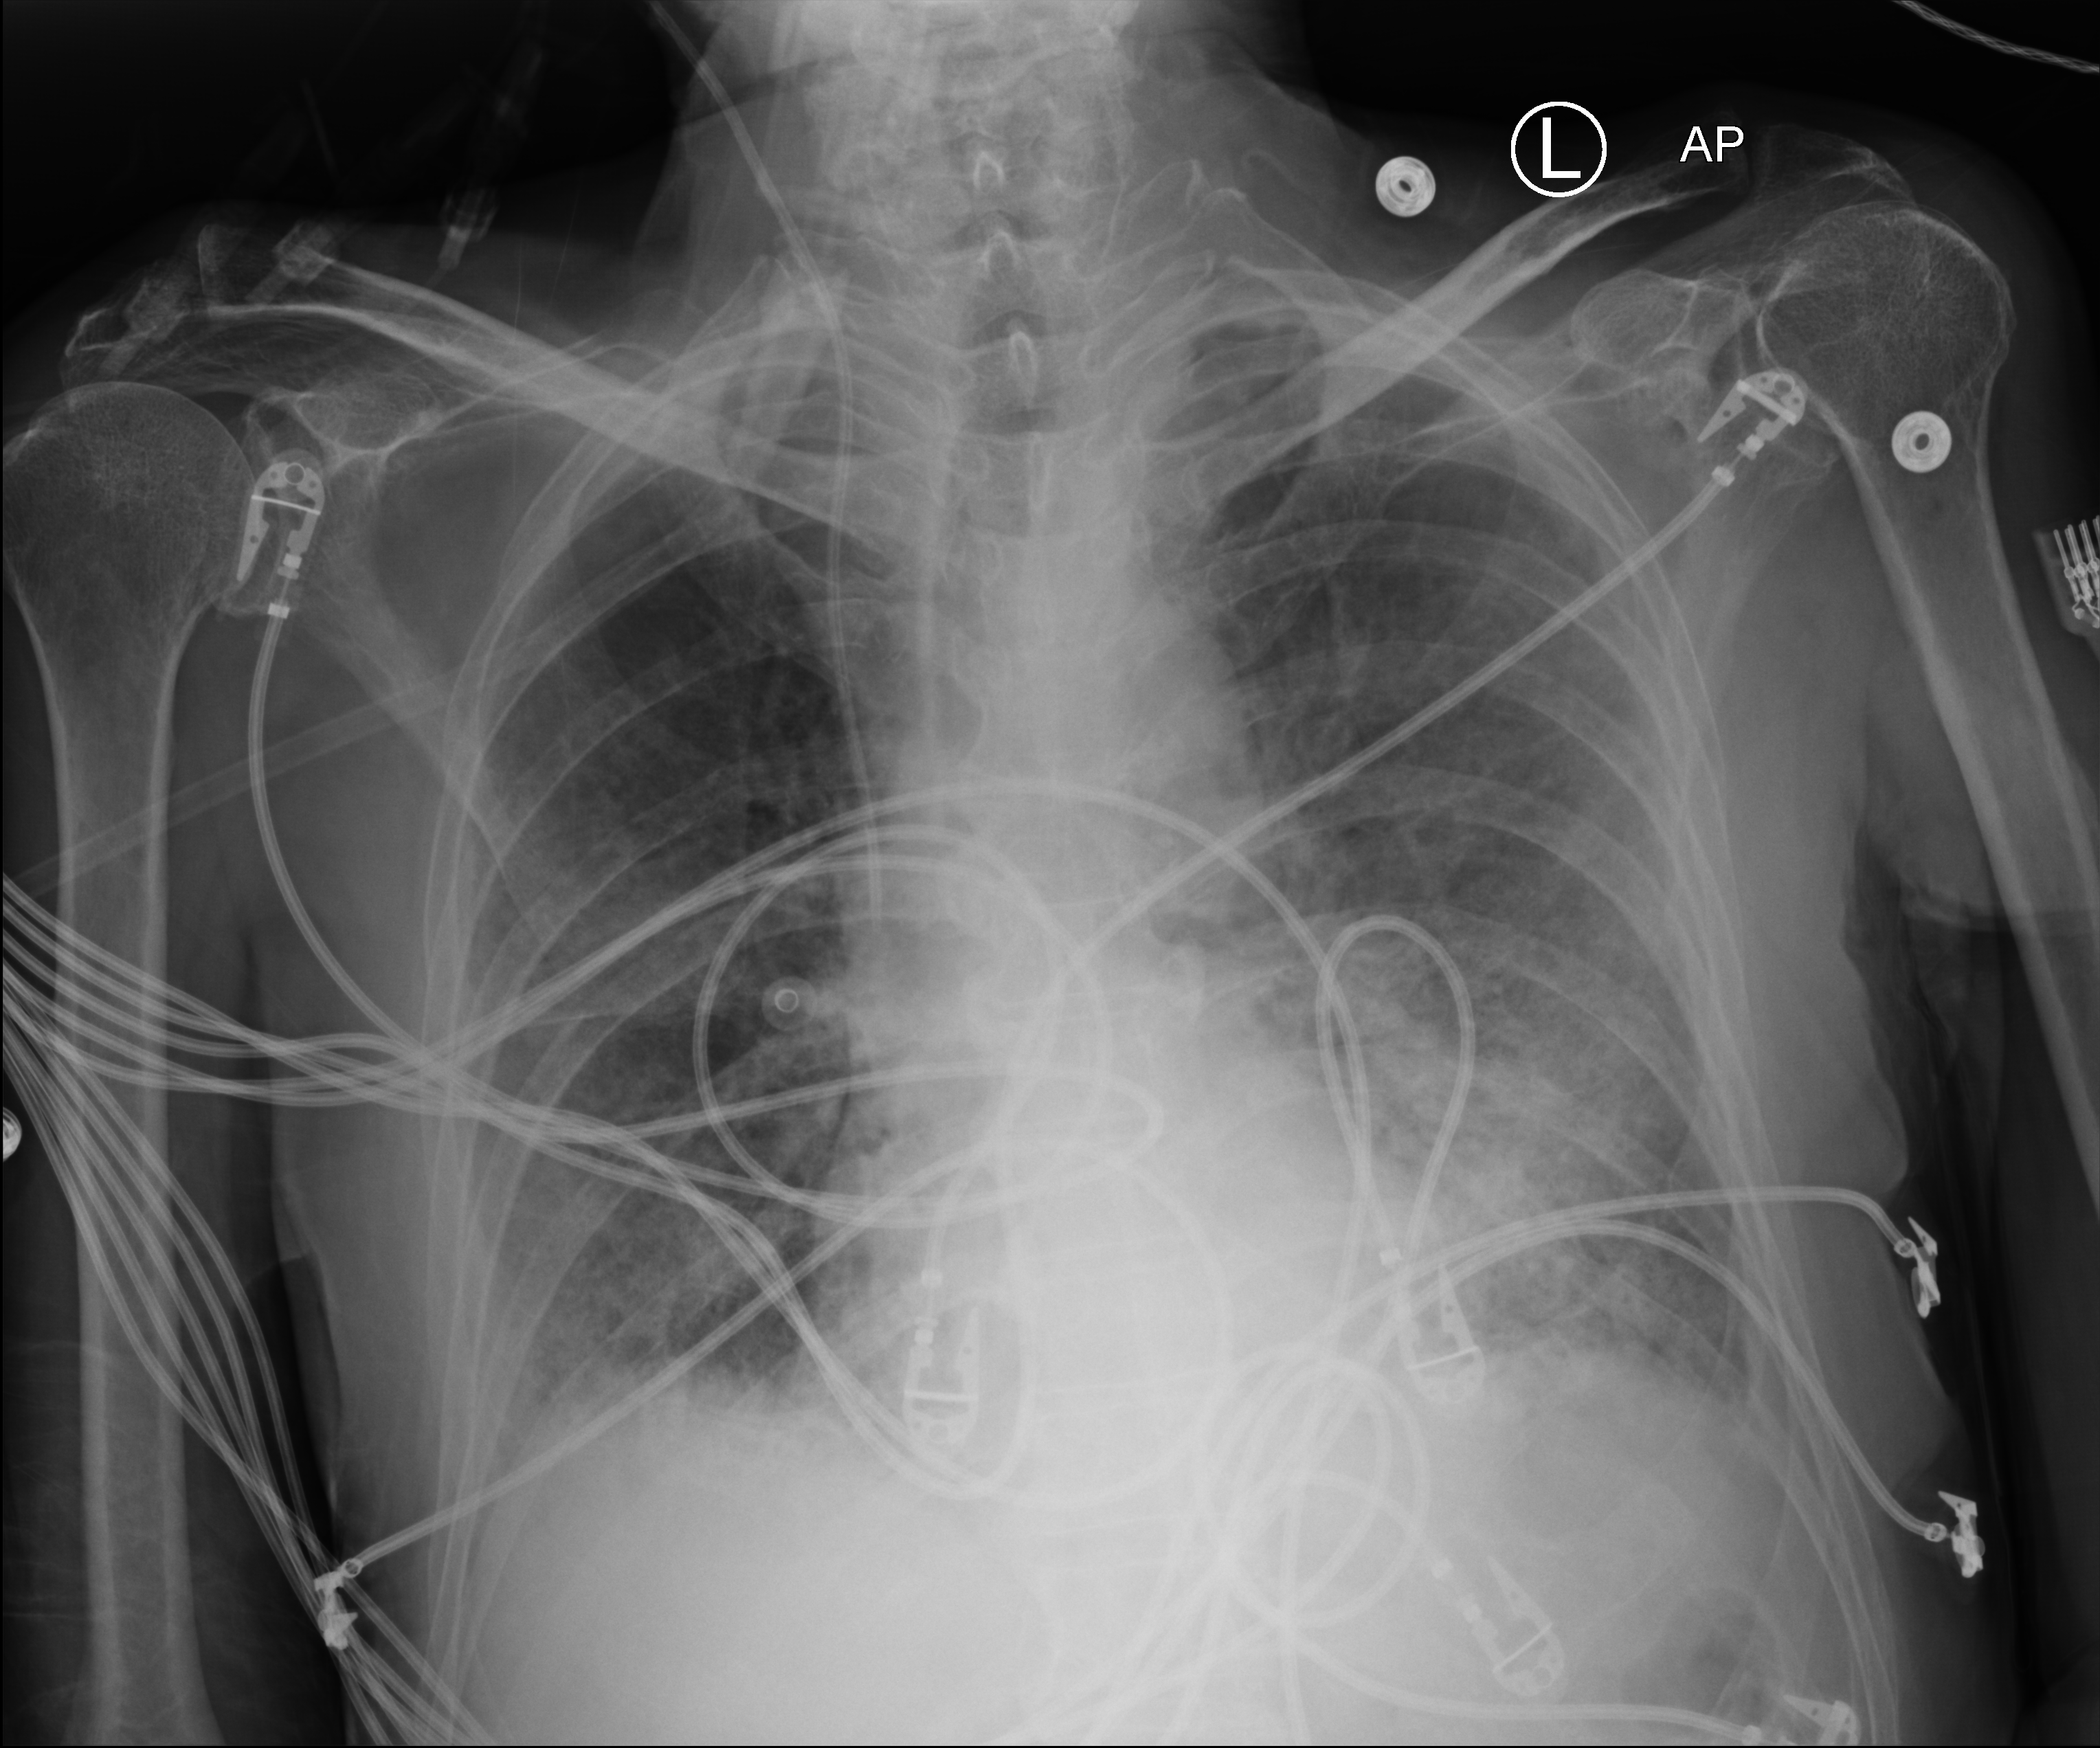
Portable chest radiograph, anteroposterior (AP) projection. Male patient hospitalised with COVID-19, age 60–74 years.
Hospital-stay facts (about this admission, not read from this image; timing relative to this image not recorded): admitted to intensive care during this hospital stay: yes.